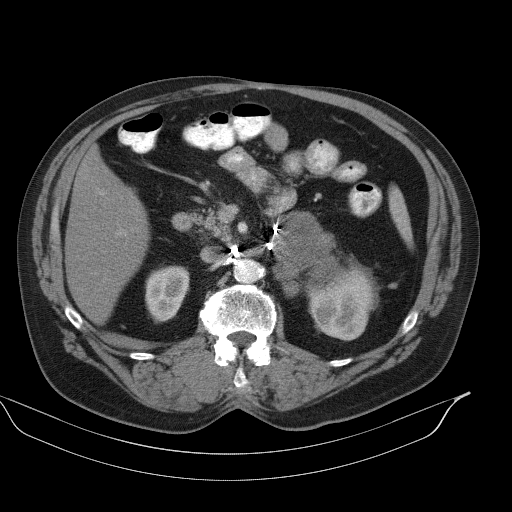
Contrast-enhanced abdominal CT, one axial slice. Slice 60 of 92 in the series (ordered by position). 130 kVp. Intravenous contrast given. Soft-tissue window (W 400 / L 40 HU). 5 mm slice thickness. 512 × 512 image matrix, field of view 449 × 449 mm. Patient: male, 56 years. Case-level facts recorded for this patient, not image findings: diagnosis: adrenocortical carcinoma; tumour side: left adrenal; tumour size at pathology: 15 cm; Ki-67 index: 35 %; stage (as recorded): 4.
Structures marked on this image (semi-automatic segmentation, software-assisted and operator-edited):
- mass: bounding box [x1, y1, x2, y2] px = [278, 213, 333, 265]